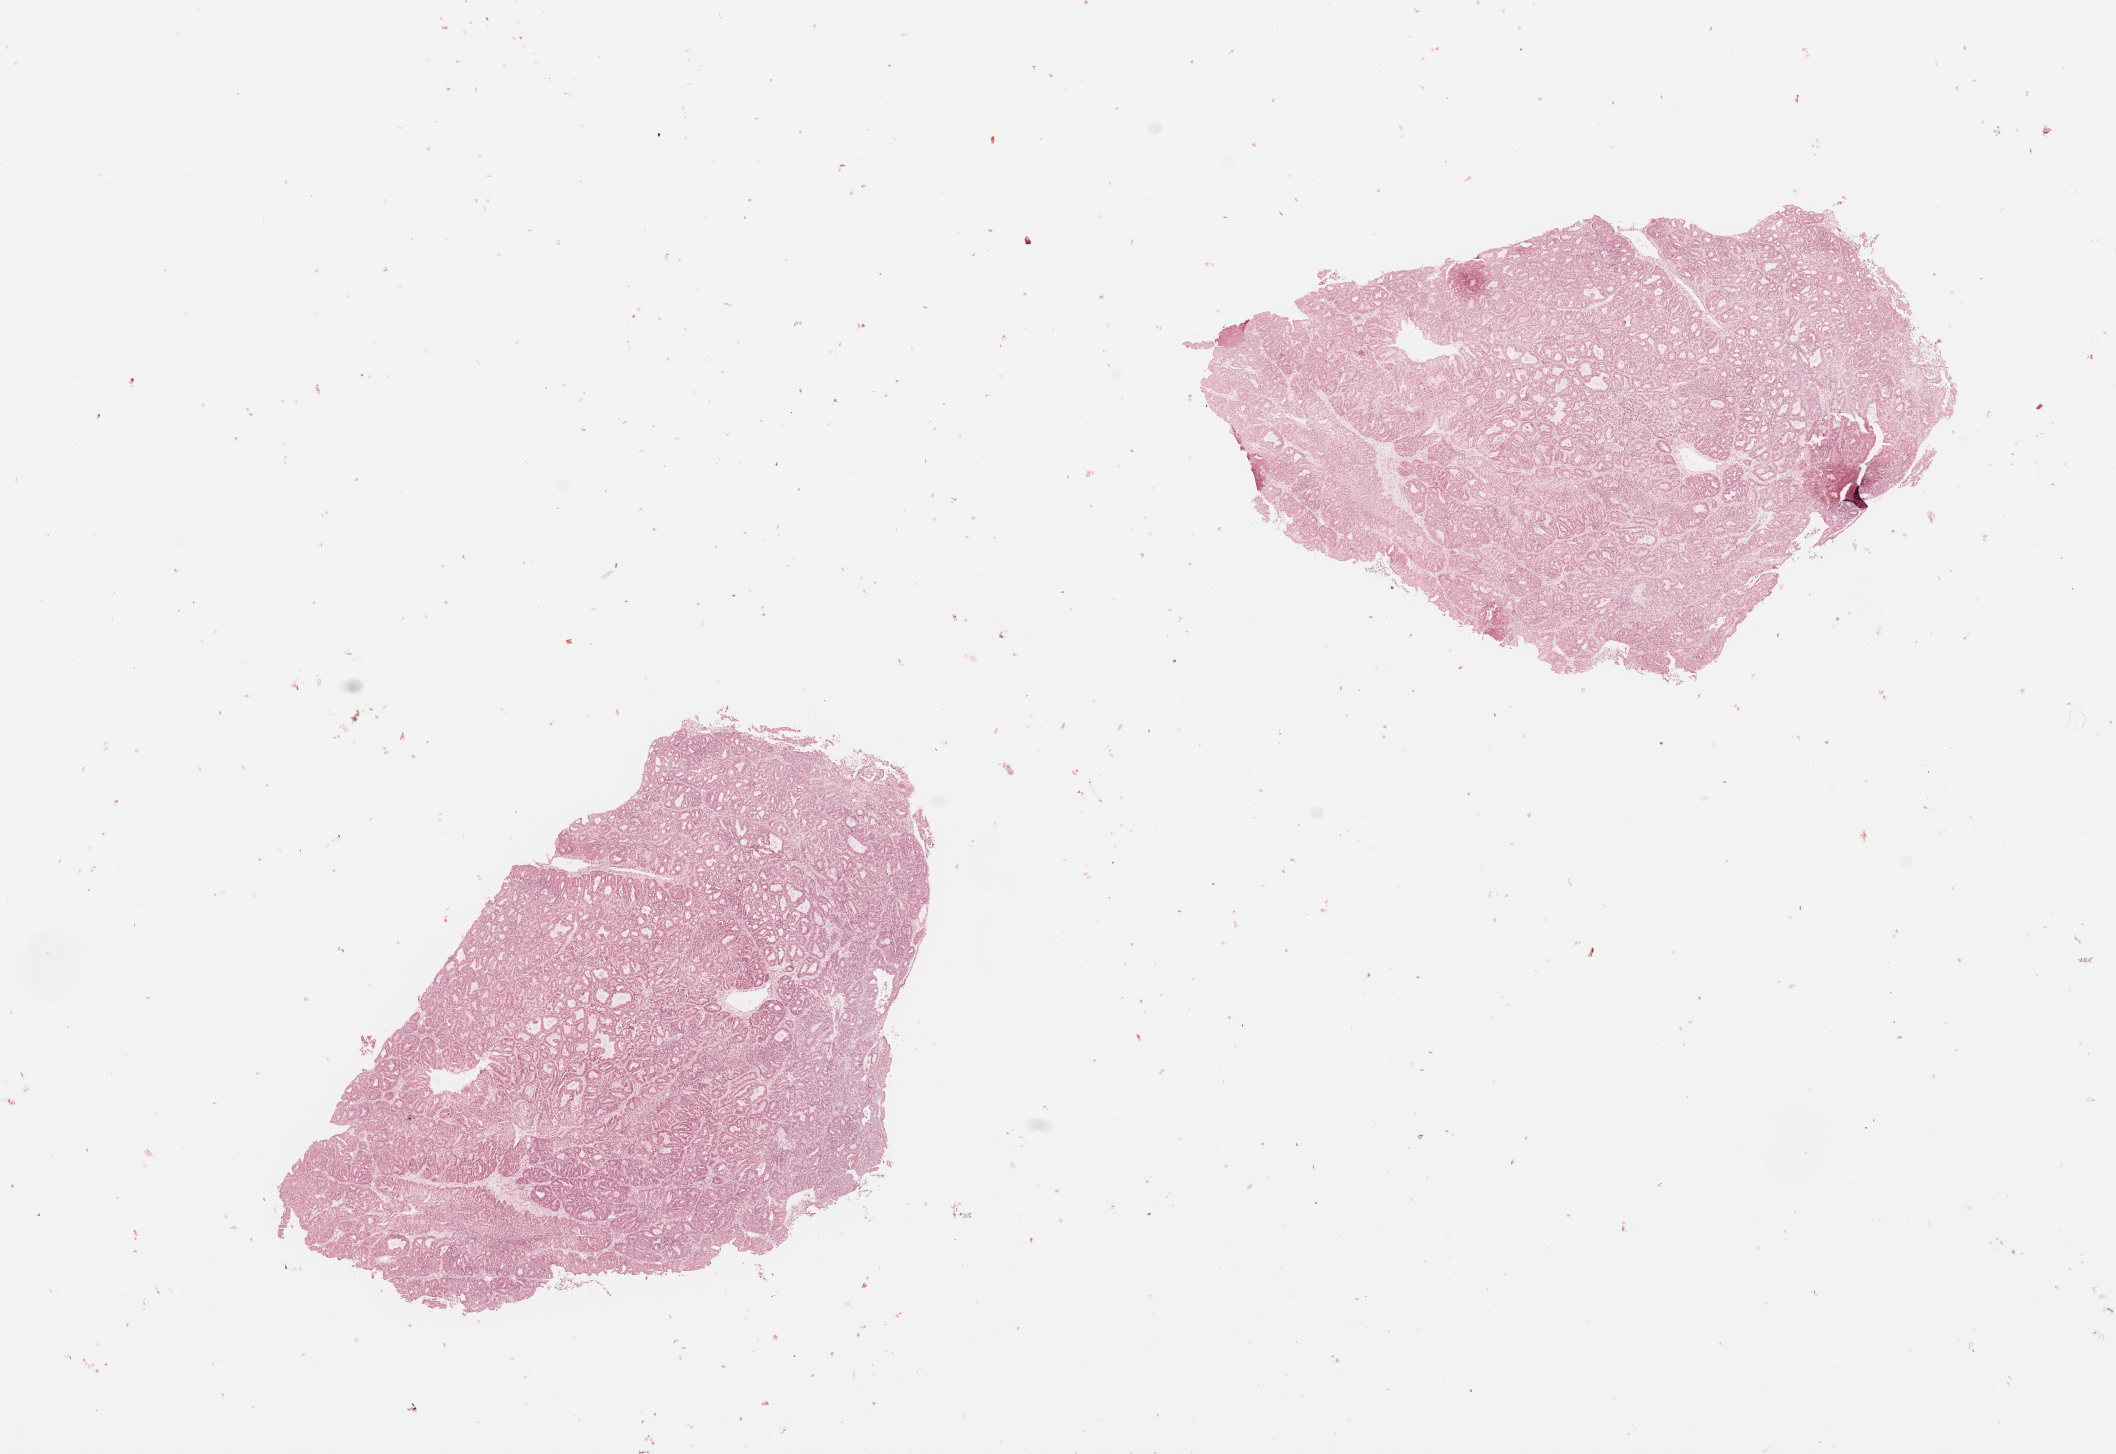
H&E whole-slide image, shown as a low-resolution overview of the whole scanned area (about 16.7 x 11.5 mm, from a 20x scan). Tumour tissue sample, uterus. 83-year-old female patient. Histologic grade: G2 (moderately differentiated).
* primary tumour site (as recorded): posterior endometrium
* AJCC pathologic stage: II
* histologic diagnosis: Endometrioid adenocarcinoma, NOS